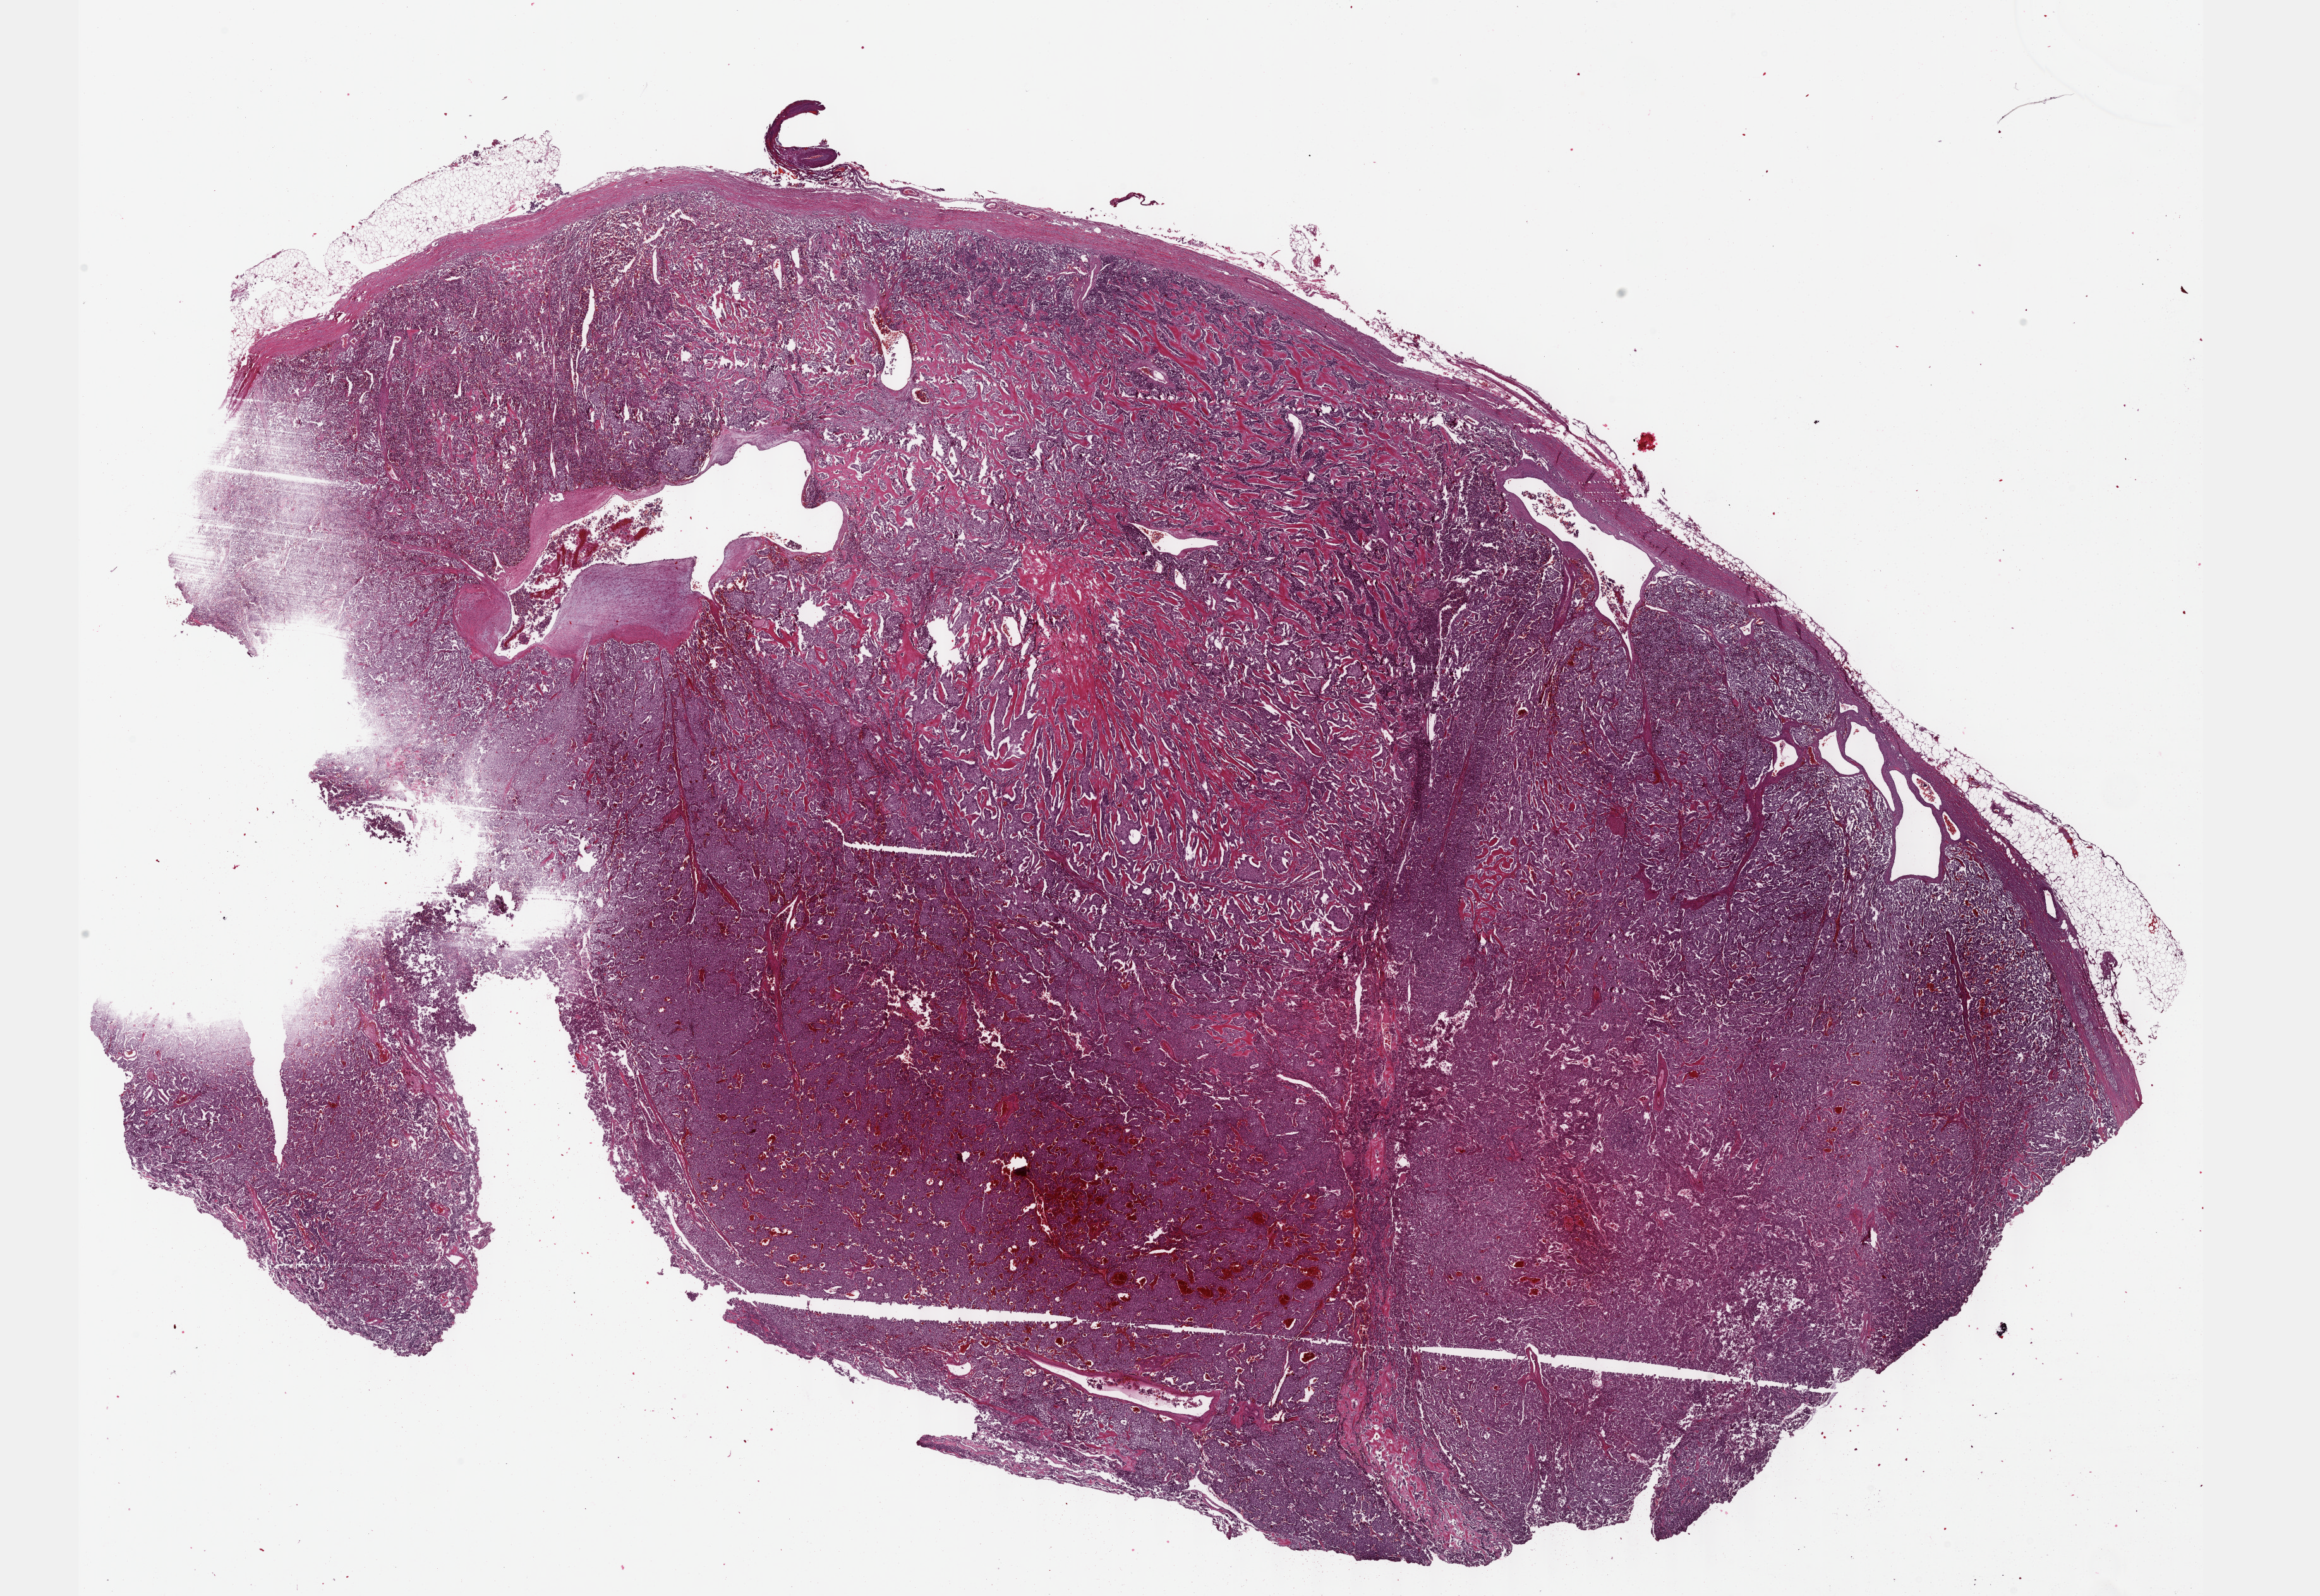
Whole-slide histology image, H&E — shown as a low-resolution overview of the whole scanned area (about 29.7 x 20.4 mm, acquisition: 40x scan); formalin-fixed paraffin-embedded (FFPE) diagnostic section; primary tumour sample from the adrenal gland. Patient: female, age at initial diagnosis 68 years.
Pathologic diagnosis: Pheochromocytoma, malignant. Laterality: right.